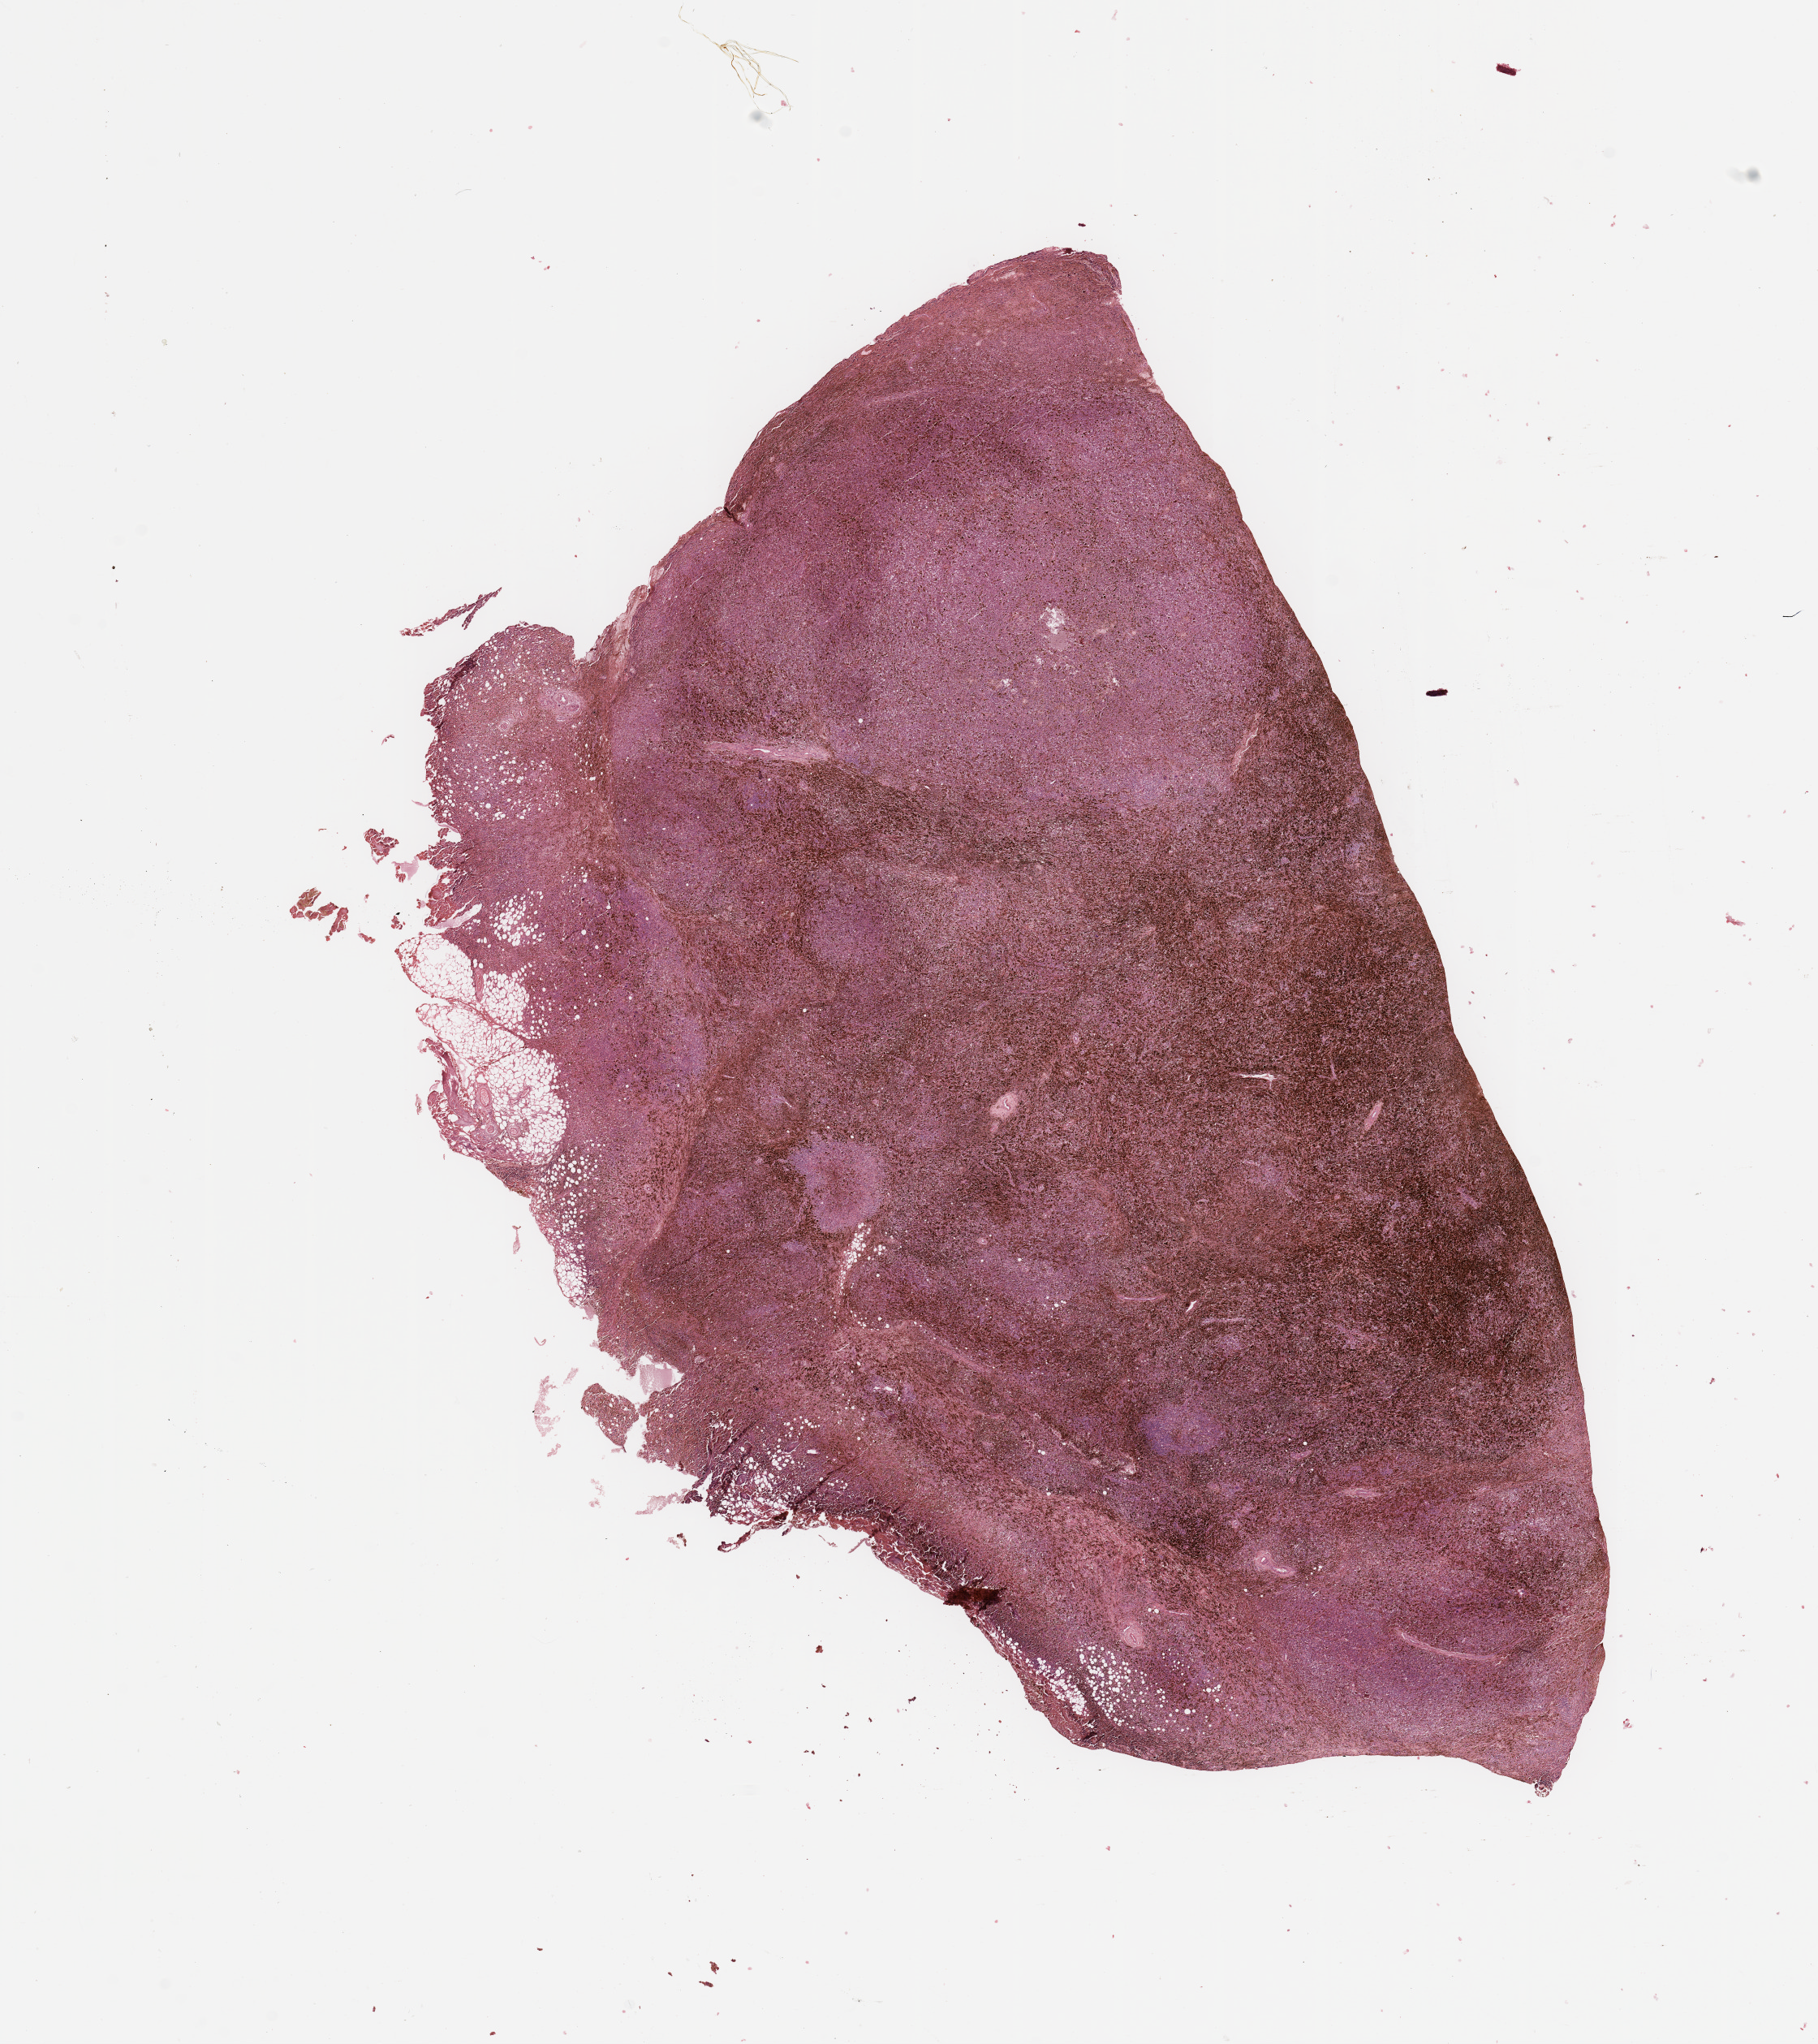
Whole-slide histology image, H&E — a low-resolution overview of the entire scanned area, about 17.7 x 19.9 mm; melanoma tumour tissue; sampled site not recorded. Patient: male, age 64 years.
• diagnosis: Malignant melanoma, NOS
• AJCC pathologic stage: IIIB